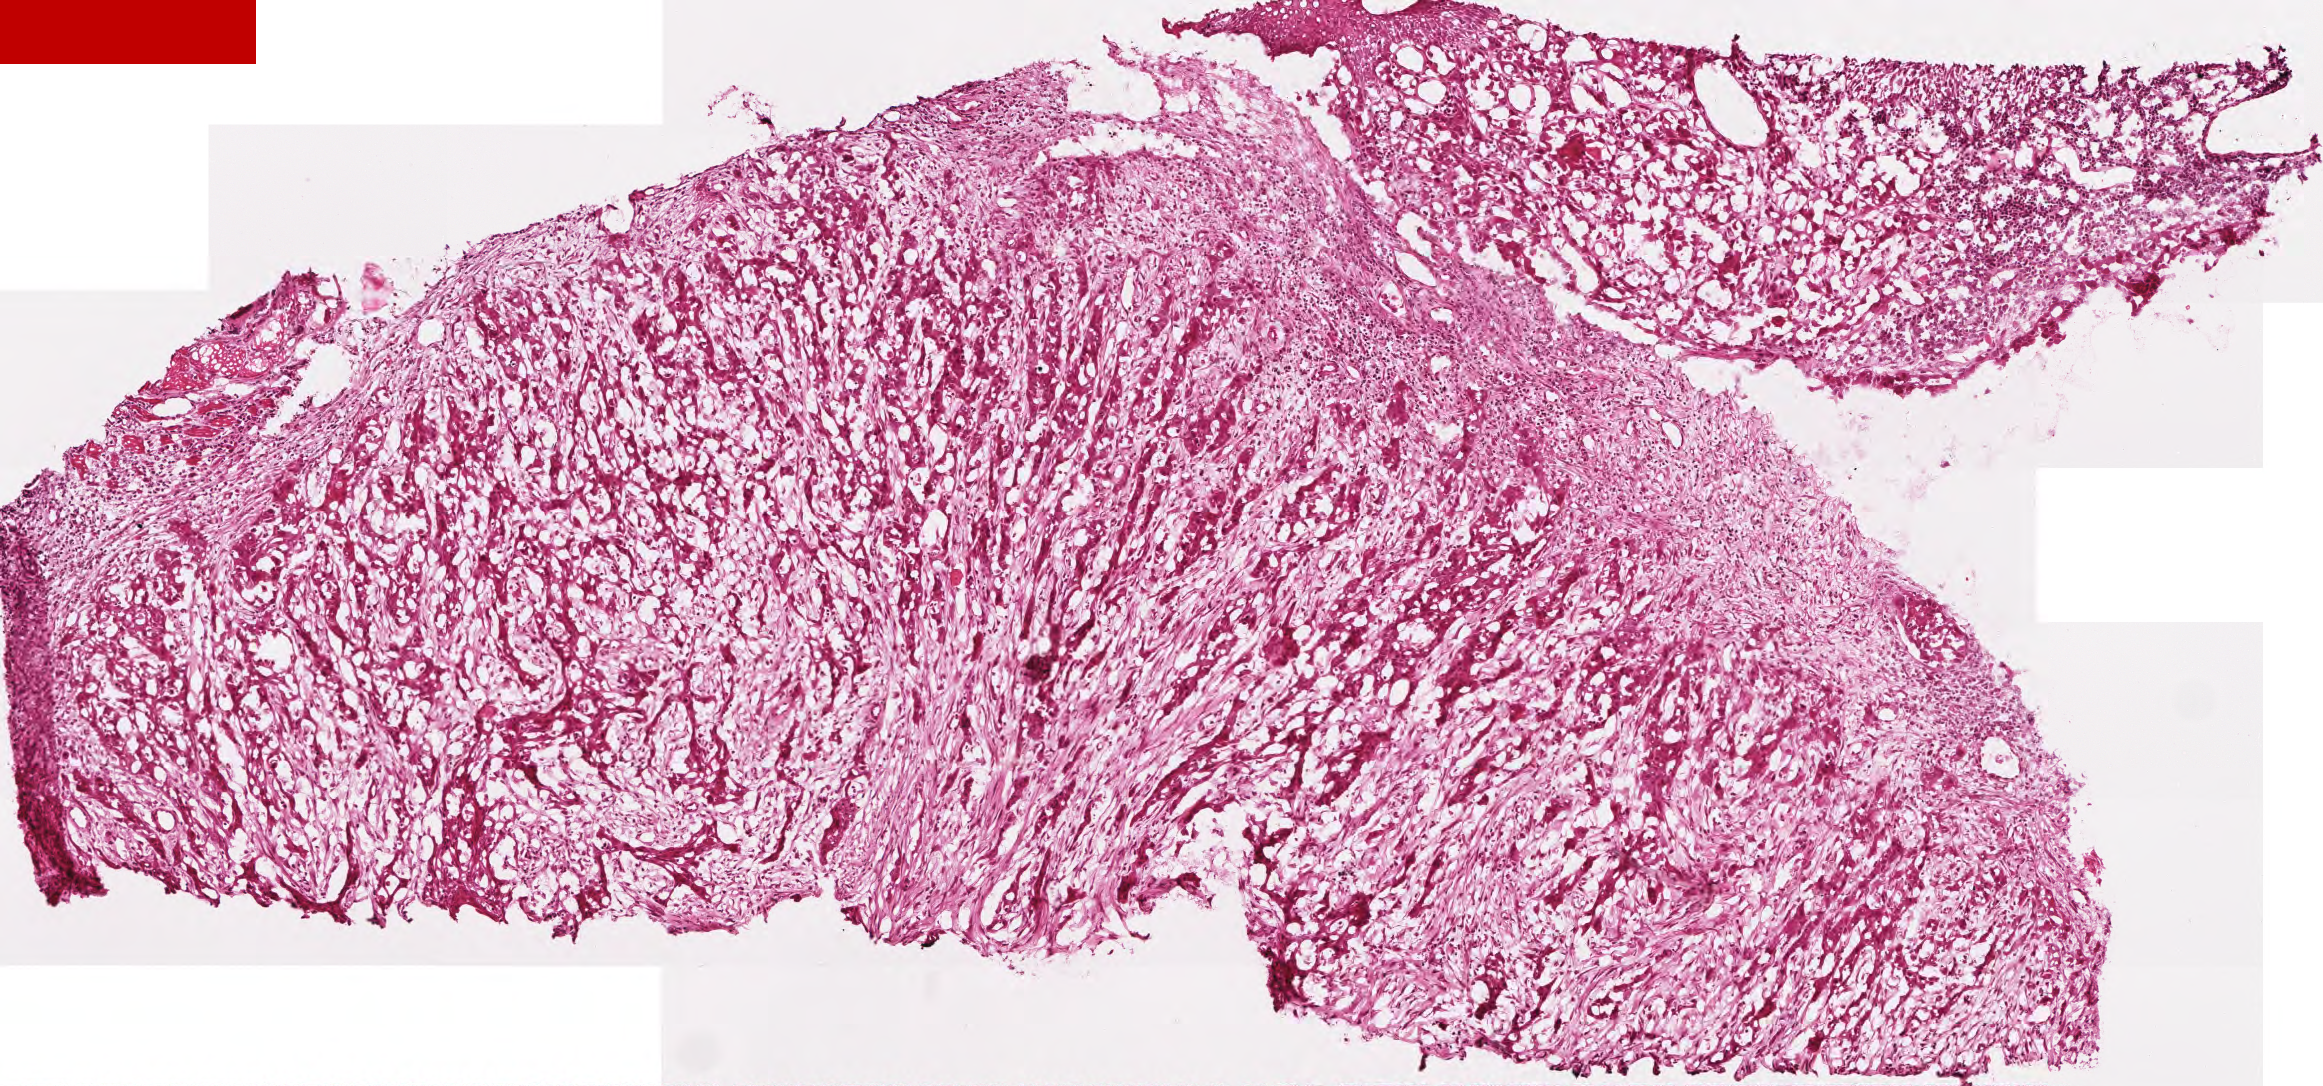
H&E whole-slide image — a low-resolution overview of the entire scanned area, about 4.6 x 2.2 mm; frozen section from the top of the tissue portion; sample: primary tumour, head and neck. Patient: female, age at initial diagnosis 79 years. Histologic grade: G2 (moderately differentiated). Composition of this section per pathologist review: tumour cells 63%, tumour nuclei 65%, normal cells 2%, stromal cells 35%, necrosis 0%. Infiltration values recorded for this section: lymphocyte infiltration 20%.
Histologic diagnosis: Squamous cell carcinoma, NOS (tonsil, NOS). Laterality: right. AJCC pathologic stage: I (6th edition).